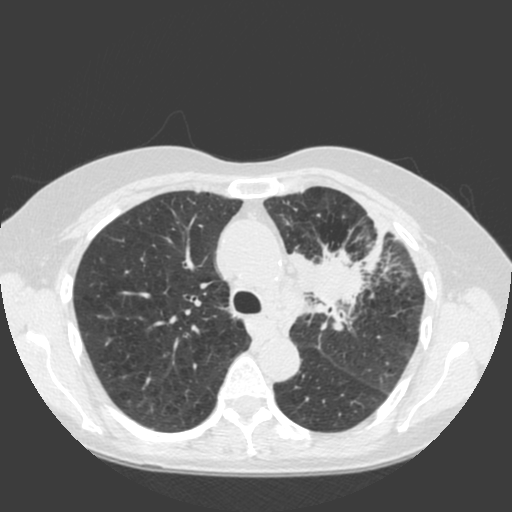
Low-dose screening chest CT, axial slice; baseline annual screen; lung window (W 1500 / L -600 HU); standard (soft-tissue) reconstruction kernel (C); 120 kVp; slice 53 of 184 in the series; 512 × 512 image matrix. Female, age 66 years at enrolment. Current smoker at enrolment.
Expert reader's lesion annotation, box from (x=284, y=233) to (x=398, y=335) px. The exam's reader record, not a measurement of the box and not confirmed to be the same lesion: non-calcified nodule or mass ≥4 mm, left upper lobe, 61 × 45 mm, spiculated (stellate) margins, soft tissue attenuation. Official screen result: positive, change unspecified: nodule(s) >= 4 mm or enlarging nodule(s), mass(es), or other non-specific abnormalities suspicious for lung cancer. Lung cancer was diagnosed 19 days after this screen: squamous cell carcinoma, keratinizing, NOS, left upper lobe, left hilum, mediastinum, left main stem bronchus, other location, poorly differentiated (G3), stage IIIB (AJCC 6th edition), 60 mm at pathology.